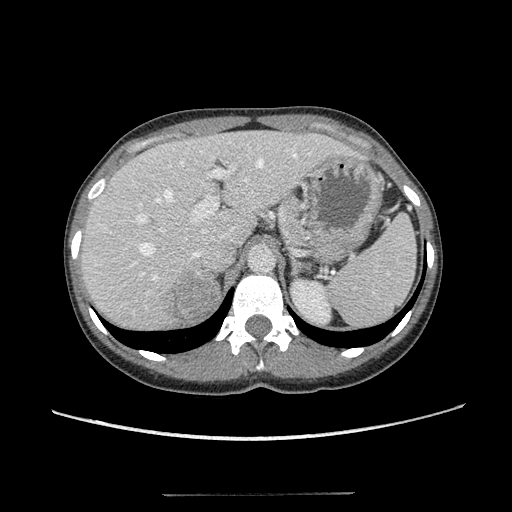
Contrast-enhanced abdominal CT, one axial slice; position 81 of 117 along the scan axis; intravenous contrast given; soft-tissue window (W 400 / L 40 HU); 2.5 mm slice thickness; 512 × 512 image matrix, field of view 365 × 365 mm. Patient: female, 35 years. From the clinical record (not read from this slice): diagnosis: adrenocortical carcinoma; tumour side: right adrenal; tumour size at pathology: 3 cm; Ki-67 index: 21 %.
Structures marked on this image (semi-automatically segmented with operator editing):
- mass: bounding box (x1, y1, x2, y2) in pixels: (162, 272, 217, 320)